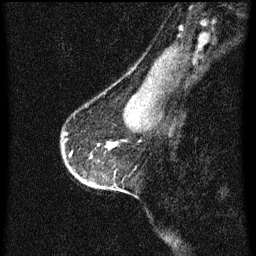
Breast MRI (dynamic contrast-enhanced), one sagittal slice. Position 50 of 60 along the scan axis. Dynamic contrast-enhanced series, image 2 of 3 at this slice position (ordered by acquisition). 1.5 T. TE 4.2 ms, TR 8 ms. 2 mm slice thickness. 256 × 256 image matrix. Female patient, age 56 years.
Outlined on this slice (semi-automatically segmented with operator editing):
- analysis volume of interest (the breast-tissue region the enhancement analysis was run in; not a lesion): bounding box <61,134,120,191> (left, top, right, bottom; pixels)
- tumour enhancement mask (voxels above the 70 % enhancement threshold inside the analysis volume of interest): <92,144,112,185>